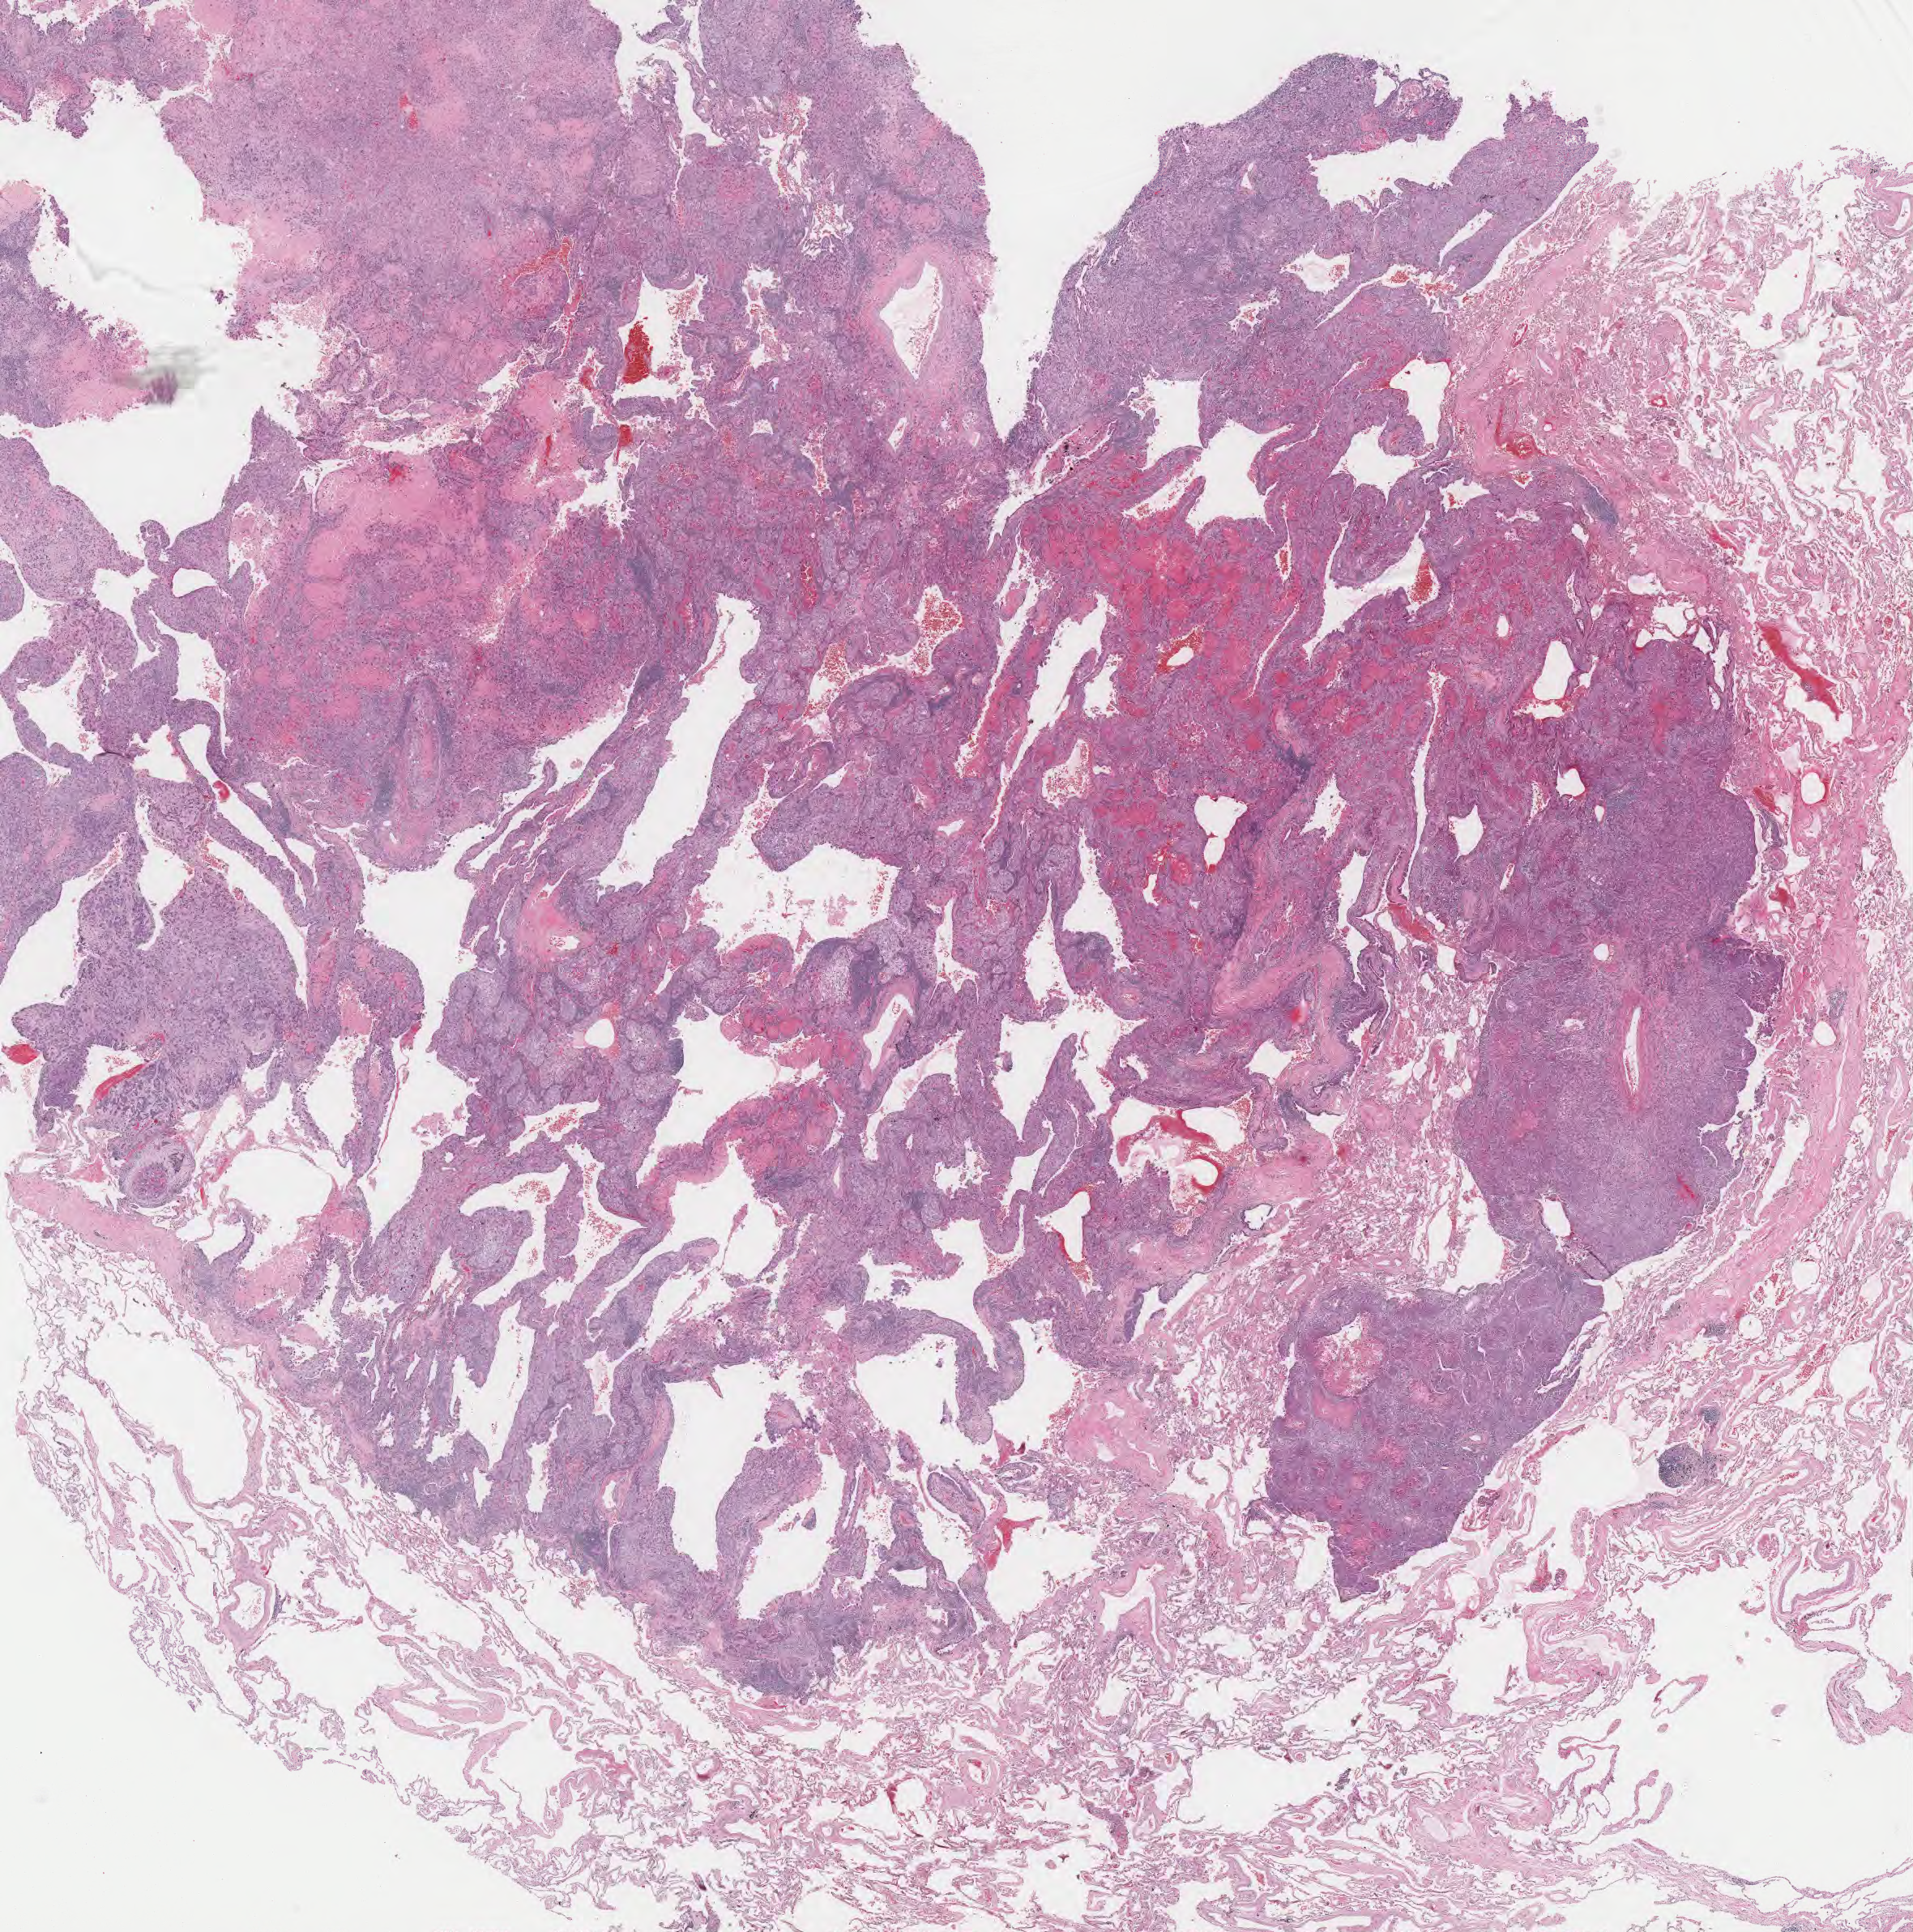
H&E whole-slide image, low-resolution overview of the scanned area, about 18.9 x 19.1 mm (from a 40x scan); FFPE section; sample: primary tumour, lung. Patient: male, age at initial diagnosis 59 years.
• AJCC pathologic stage: IIIA (7th edition)
• pathologic diagnosis: Squamous cell carcinoma, NOS (upper lobe, lung)